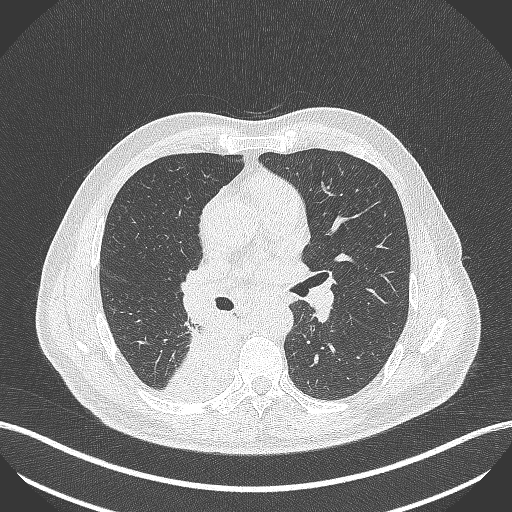
Chest CT, one axial slice. Slice 261 of 451 in the series (ordered by position). 100 kVp. Lung window (W 1500 / L -600 HU). 1 mm slice thickness. 512 × 512 image matrix, field of view 400 × 400 mm. Patient: male, 61 years. From the clinical record (not read from this slice): clinical TNM (as recorded): T1 N0 M0; histopathological grade: G3.
Structures marked on this image (rectangle marked by the reading radiologist):
- lung tumour (recorded histology: small cell carcinoma): bounding box <157,306,237,404> (left, top, right, bottom; pixels)